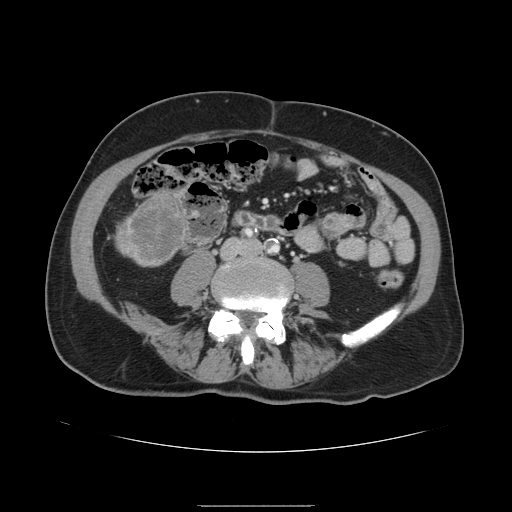
Contrast-enhanced abdominal CT, one axial slice; position 14 of 168 along the scan axis; soft-tissue window (W 400 / L 40 HU); 2.5 mm slice thickness; 512 × 512 image matrix, field of view 386 × 386 mm. Male patient, age 74 years. From the clinical record (not read from this slice): diagnosis: colorectal cancer liver metastases, imaged before liver resection; multiple liver metastases: no.
Annotated regions visible in this slice (manually delineated by an expert):
- liver: bounding box [x1, y1, x2, y2] px = [116, 190, 190, 267]
- liver metastasis: [121, 194, 187, 263]